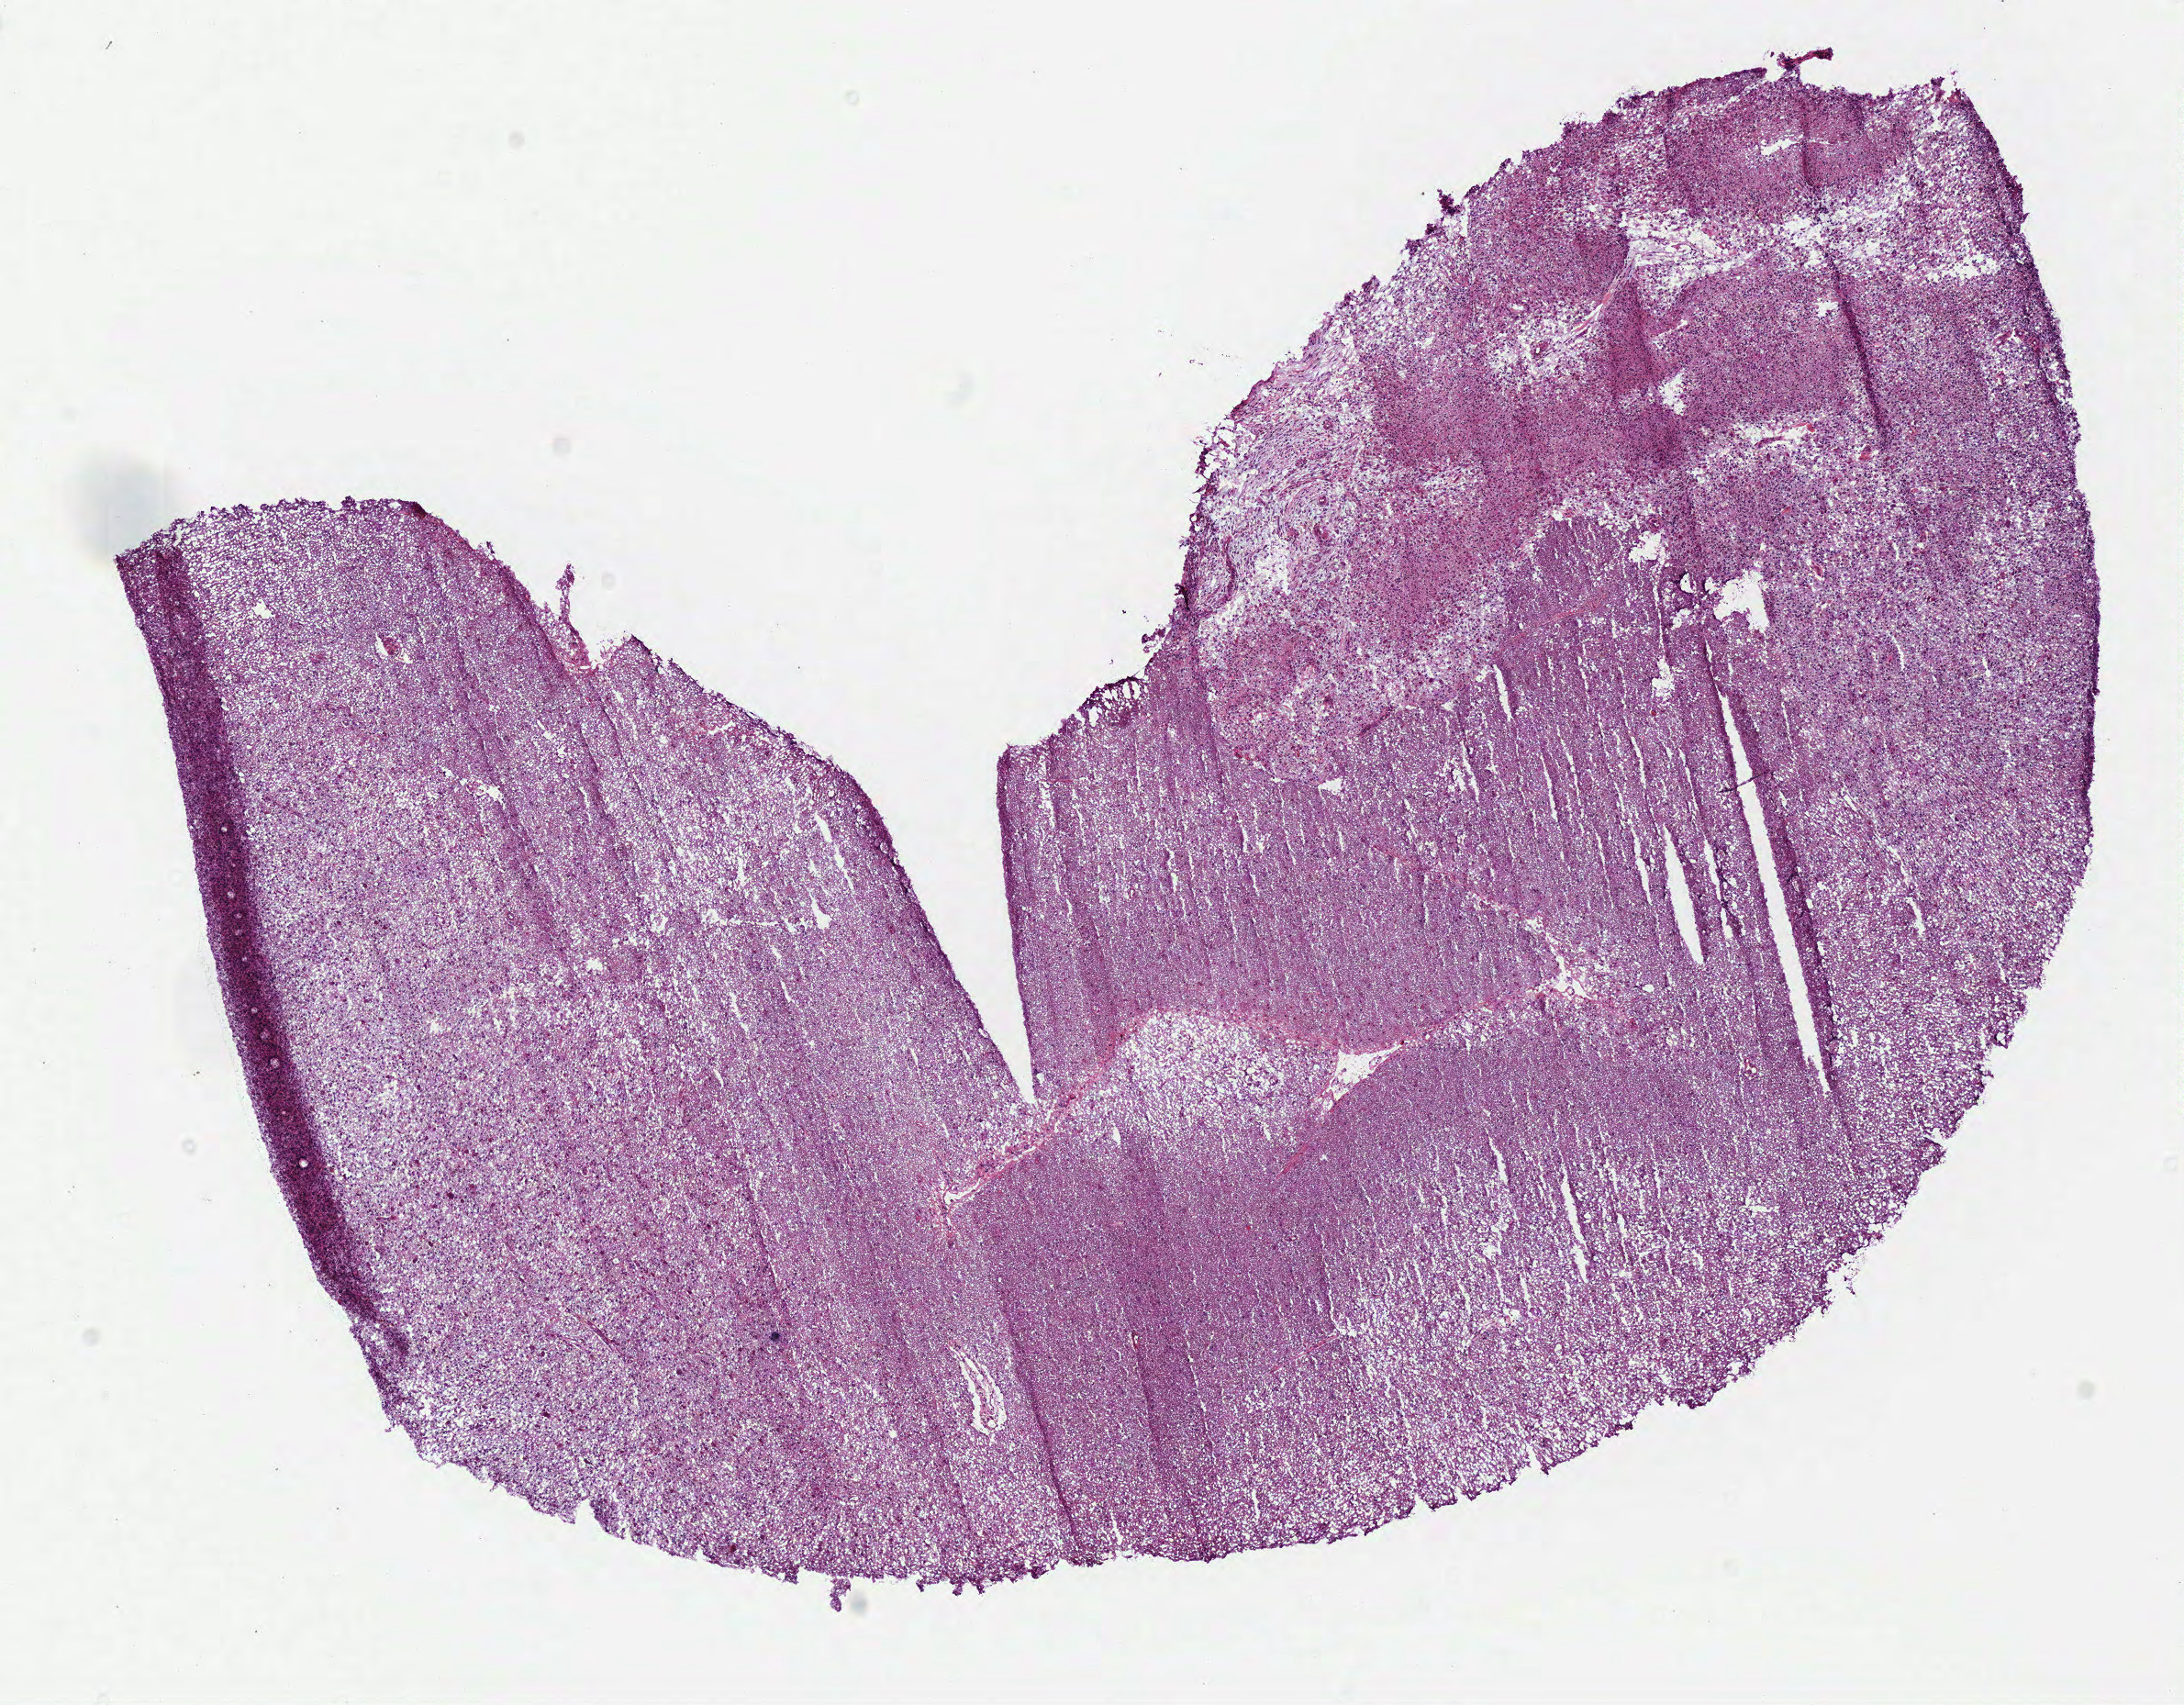
Whole-slide histology image, Hematoxylin and eosin (H&E) stained, a low-resolution overview of the entire scanned area, about 9.4 x 7.3 mm, frozen section, sample: primary tumour, brain. Patient: female, age at initial diagnosis 65 years. Pathologist review of this section (percent, as recorded): tumour cells 100%, tumour nuclei 65%, normal cells 0%, stromal cells 0%, necrosis 0%.
Pathologic diagnosis: Glioblastoma.